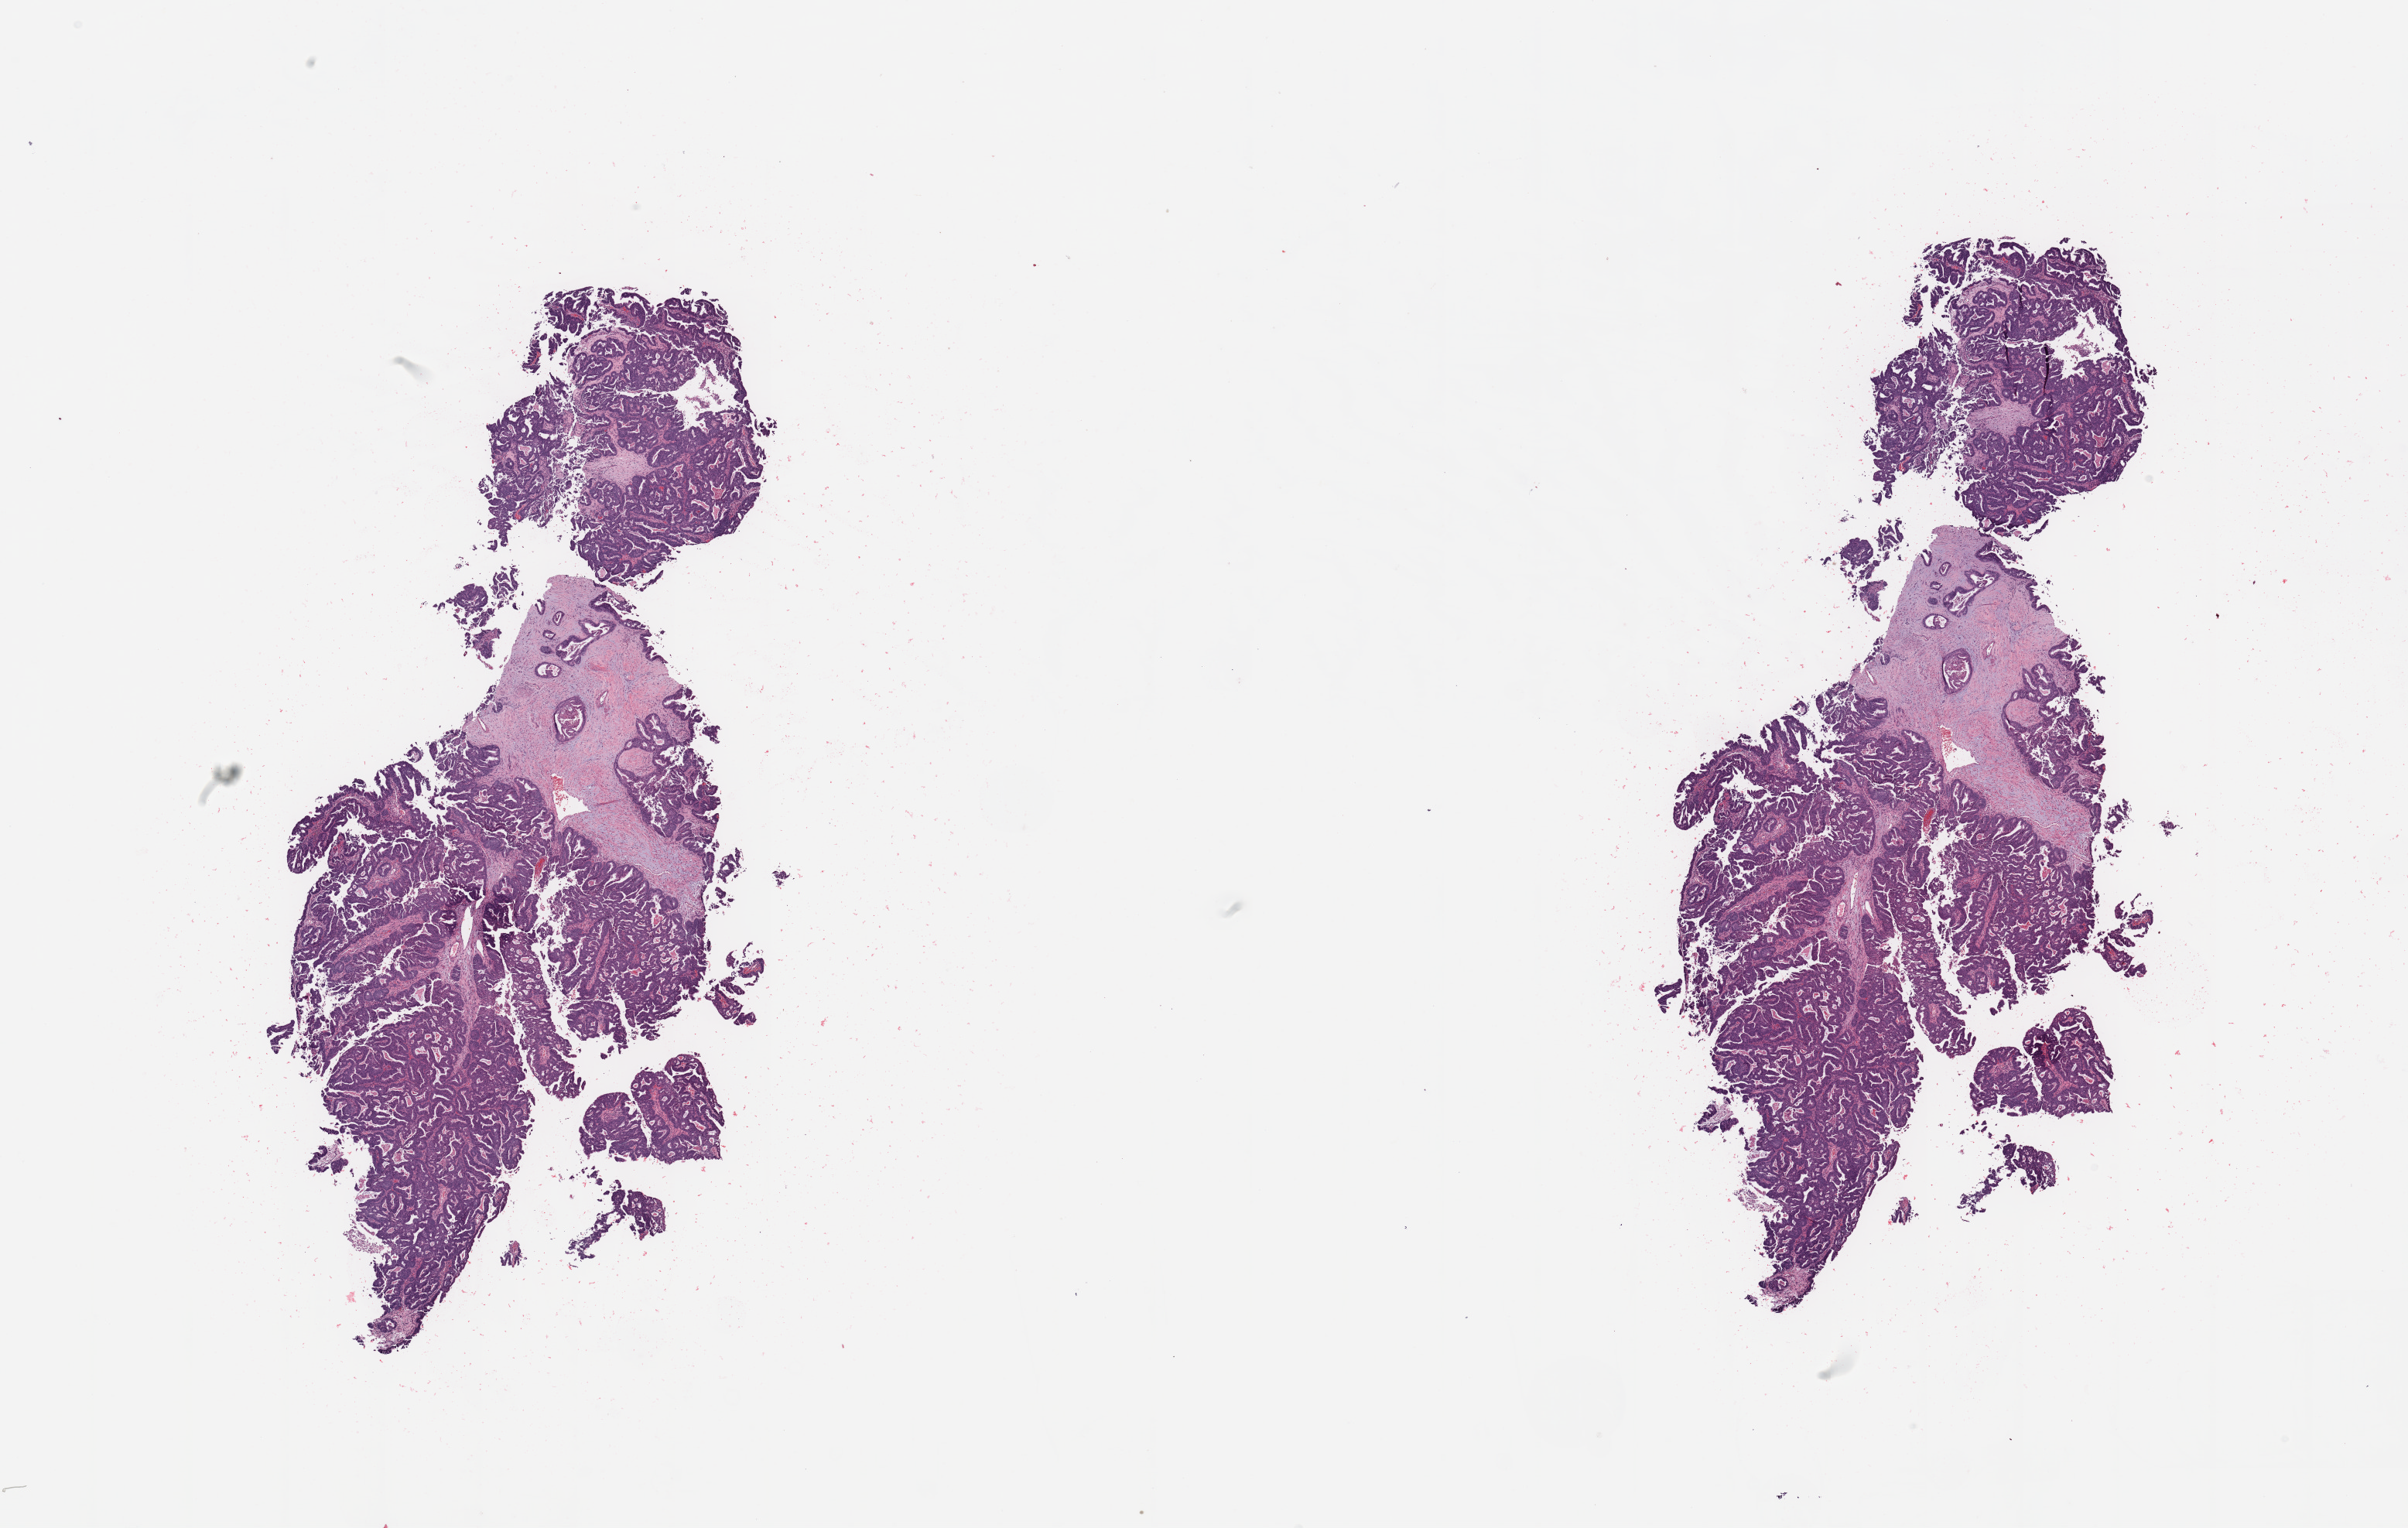
H&E-stained whole-slide image, a low-resolution overview of the entire scanned area, about 24.6 x 15.6 mm (acquisition: 20x scan), tumour tissue sample, sampled site: uterus. 64-year-old female patient. Histologic grade: G2 (moderately differentiated). Composition of this section per pathologist review: tumour nuclei 85%, necrosis 0%.
- primary tumour site (as recorded): anterior endometrium
- histologic diagnosis: Endometrioid adenocarcinoma, NOS